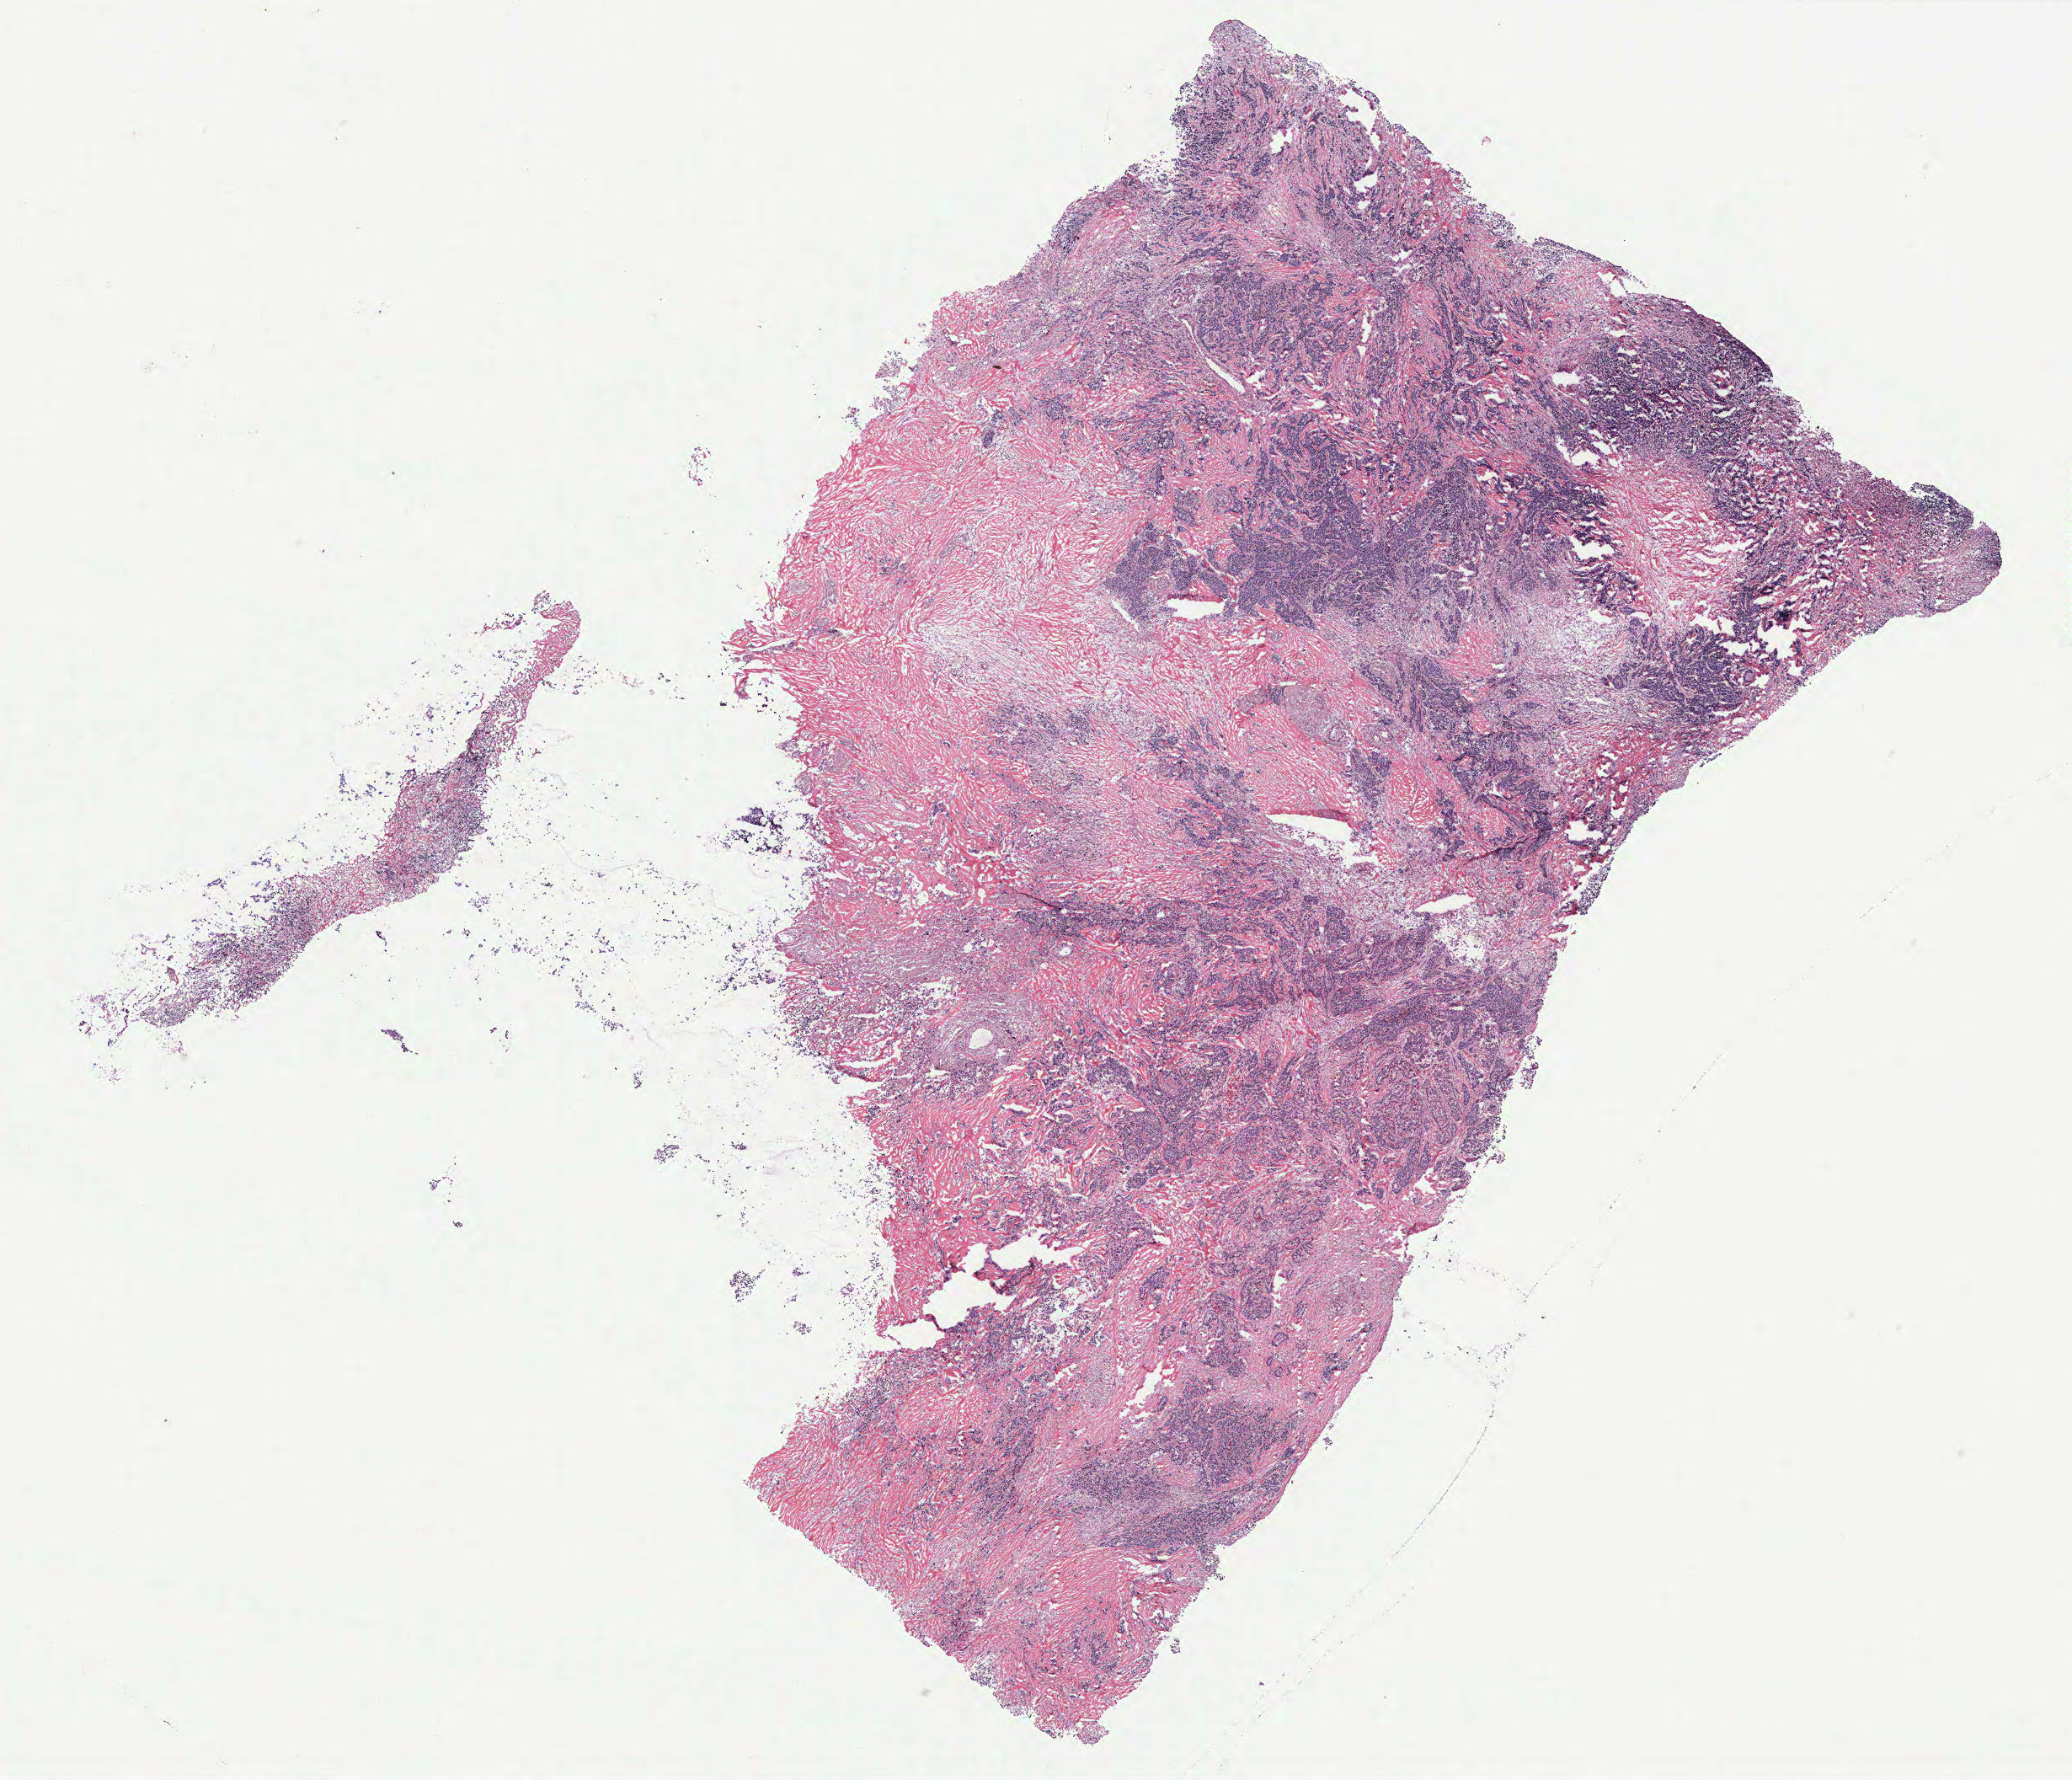
Whole-slide histology image, Hematoxylin and eosin (H&E) stained — low-resolution overview of the scanned area, about 19.7 x 16.9 mm, breast, tumour tissue. 65-year-old female patient.
Histologic diagnosis: Infiltrating duct carcinoma, NOS. AJCC pathologic stage: IIIA.